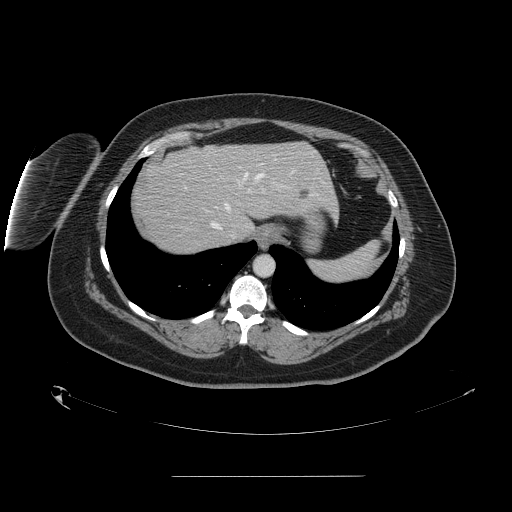
Contrast-enhanced abdominal CT, one axial slice. Slice 128 of 164 in the series (ordered by position). Intravenous contrast given. Soft-tissue window (W 400 / L 40 HU). 2.5 mm slice thickness. 512 × 512 image matrix. Female patient, age 52 years. Case-level facts recorded for this patient, not image findings: diagnosis: colorectal cancer liver metastases, imaged before liver resection; multiple liver metastases: yes; largest metastasis: 3.5 cm; chemotherapy before resection: no.
Annotated regions visible in this slice (manually delineated by an expert):
- hepatic veins: bounding box <211,172,263,239> (left, top, right, bottom; pixels)
- liver: <133,142,336,256>
- planned liver remnant (the part of the liver to remain after resection): <171,142,336,229>
- liver metastasis: <301,191,308,199>